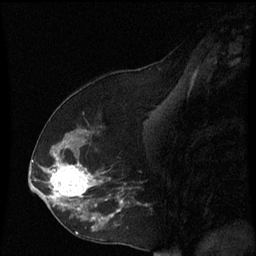
Breast MRI (dynamic contrast-enhanced), one sagittal slice; position 34 of 60 along the scan axis; dynamic contrast-enhanced series, image 2 of 3 at this slice position (ordered by acquisition); 1.5 T; TE 4.2 ms, TR 8.9 ms; 2 mm slice thickness; 256 × 256 image matrix. Female patient, age 53 years. Case-level facts recorded for this patient, not image findings: setting: breast cancer imaged before/during neoadjuvant chemotherapy; receptor status: HR-positive, HER2-negative.
Outlined on this slice (semi-automatic segmentation, software-assisted and operator-edited):
- analysis volume of interest (the breast-tissue region the enhancement analysis was run in; not a lesion): bounding box [x1, y1, x2, y2] px = [38, 128, 125, 231]
- tumour enhancement mask (voxels above the 70 % enhancement threshold inside the analysis volume of interest): [48, 162, 125, 229]